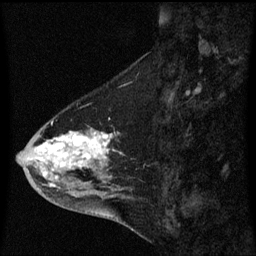
Breast MRI (dynamic contrast-enhanced), one sagittal slice. Slice 24 of 60 in the series (ordered by position). Dynamic contrast-enhanced series, image 2 of 3 at this slice position (ordered by acquisition). 1.5 T. TE 4.2 ms, TR 8.4 ms. 2 mm slice thickness. 256 × 256 image matrix, field of view 200 × 200 mm. Patient: female, 46 years. From the clinical record (not read from this slice): setting: breast cancer imaged before/during neoadjuvant chemotherapy; receptor status: HER2-positive.
Annotated regions visible in this slice (semi-automatic segmentation, software-assisted and operator-edited):
- analysis volume of interest (the breast-tissue region the enhancement analysis was run in; not a lesion): bounding box (x1, y1, x2, y2) in pixels: (18, 116, 122, 195)
- tumour enhancement mask (voxels above the 70 % enhancement threshold inside the analysis volume of interest): (43, 132, 112, 185)